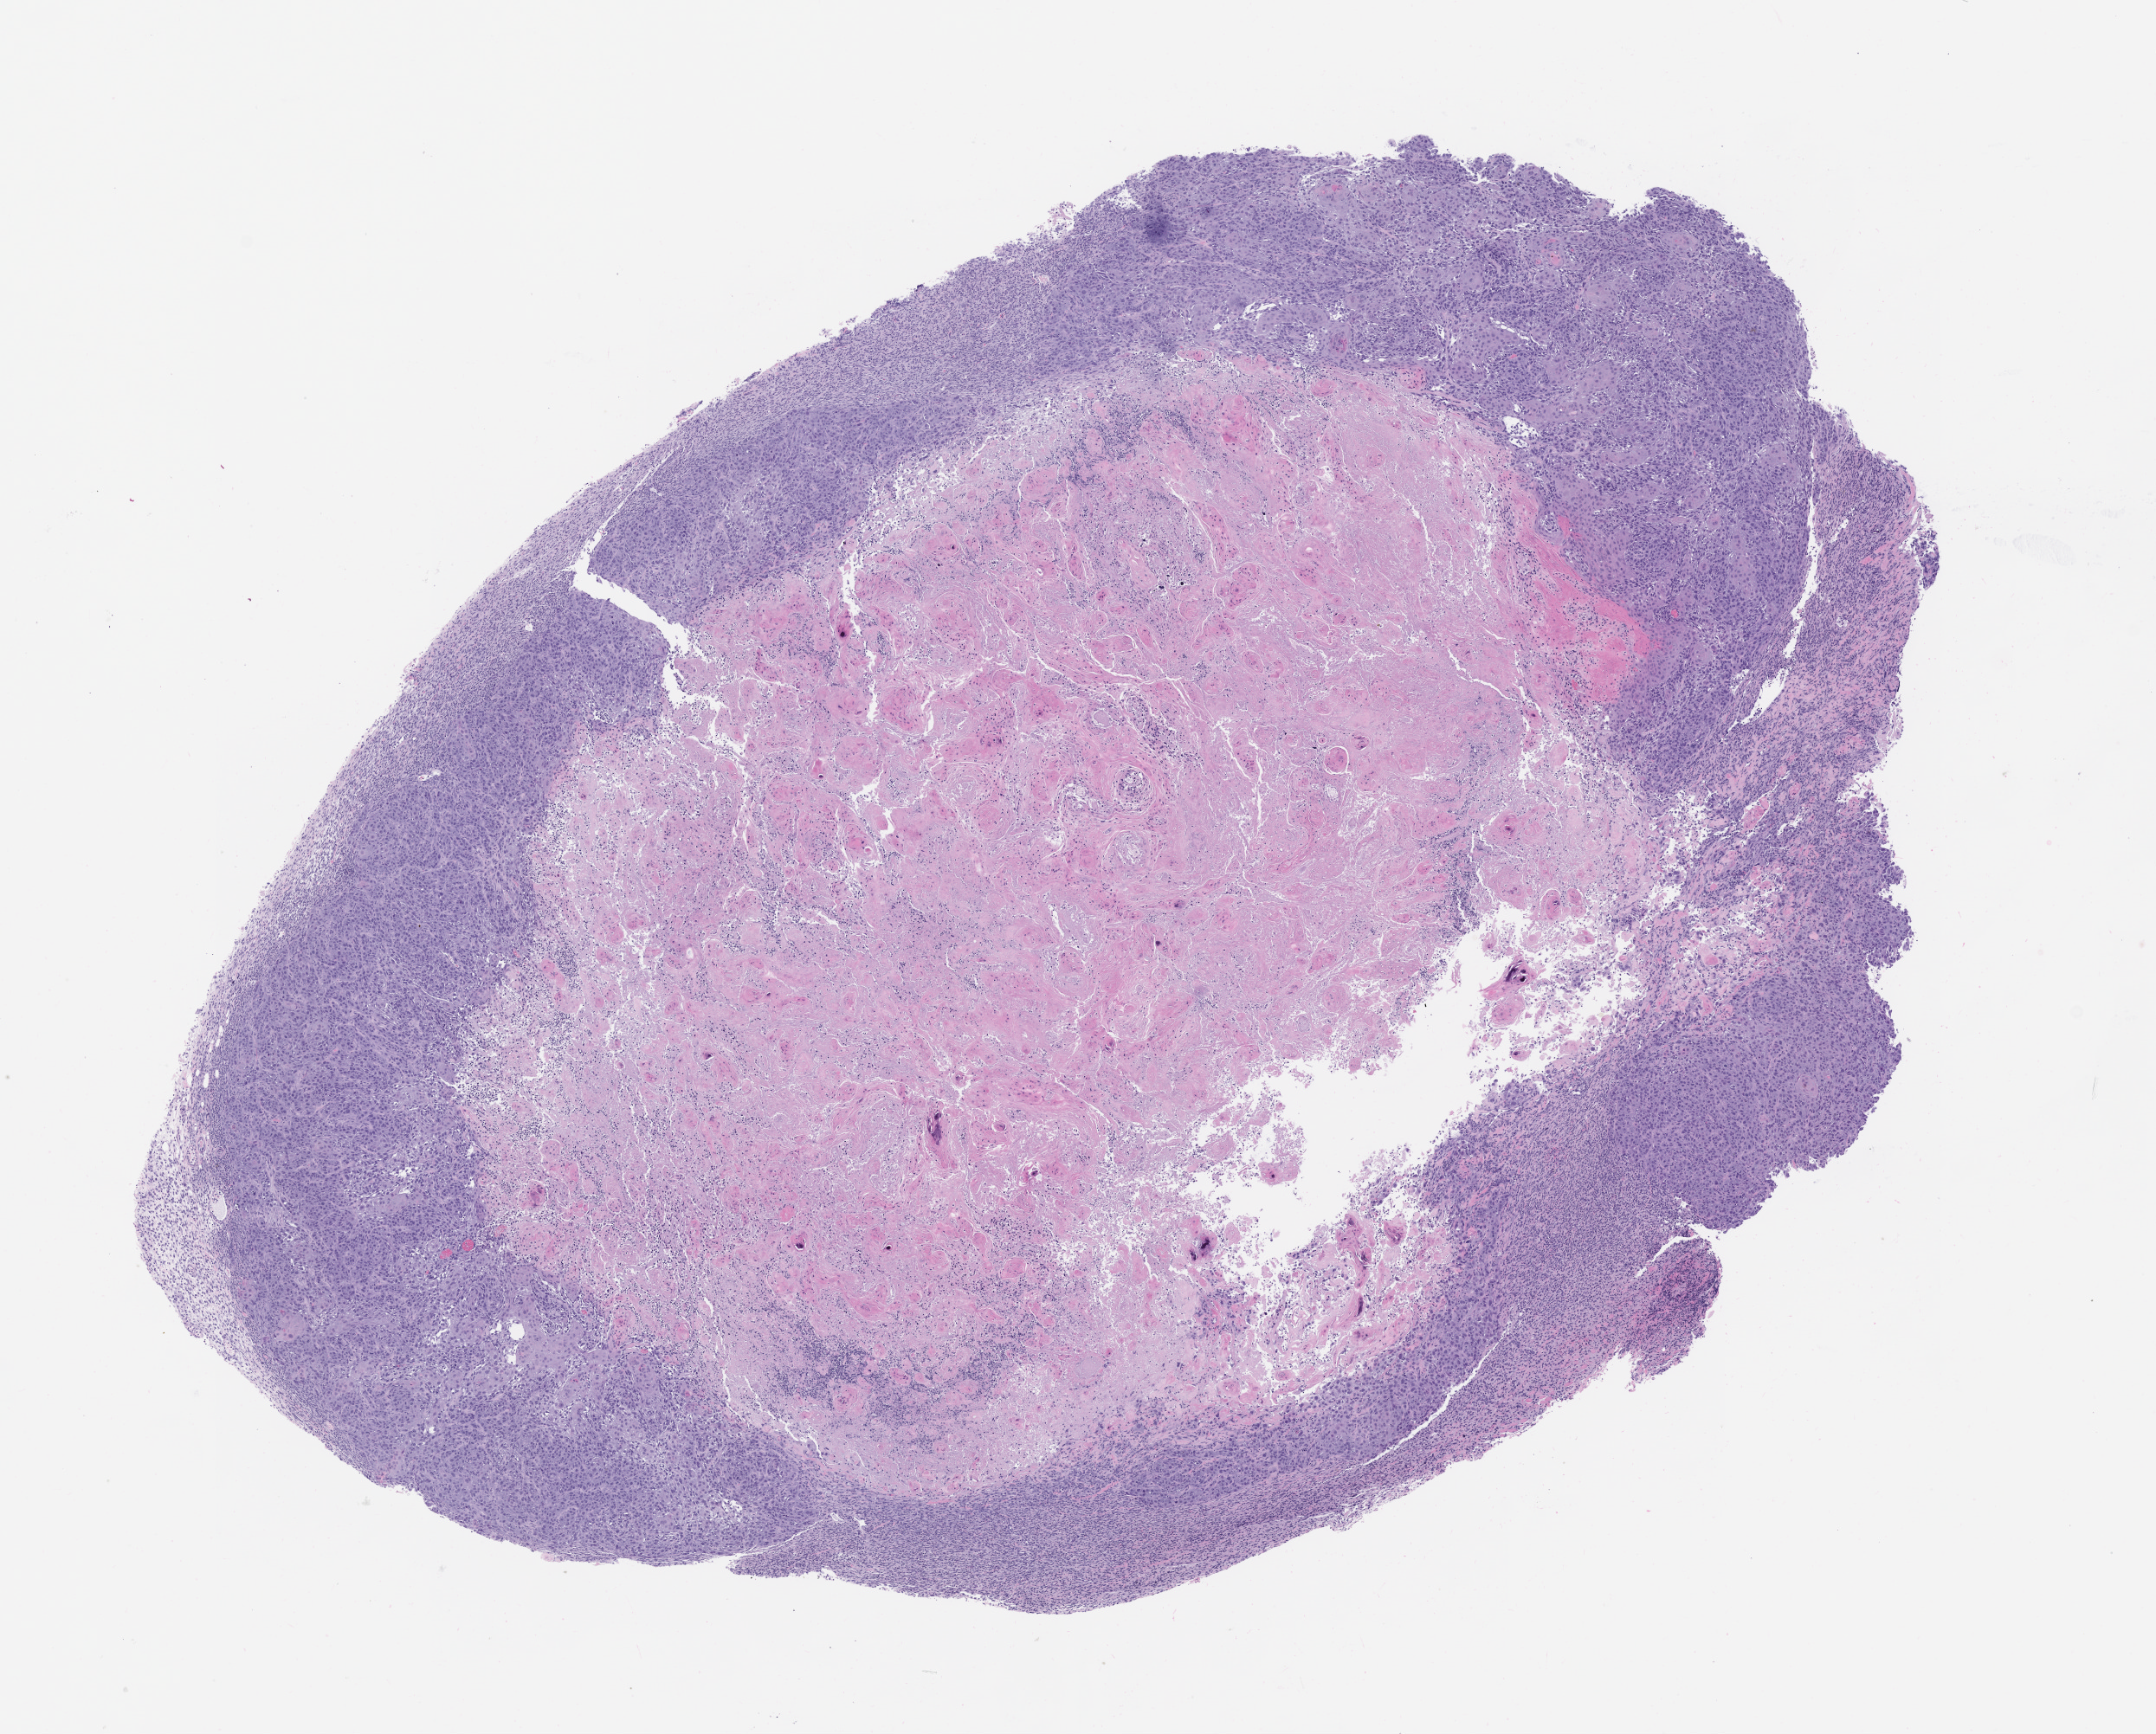
Whole-slide image, H&E: patient-derived xenograft (human tumor grown in a mouse), passage 1 — a low-resolution overview of the entire scanned area, about 10.0 x 8.1 mm, formalin-fixed, paraffin-embedded (FFPE) tissue, tumor site category: oral soft tissue.
Originating patient diagnosis: Head and Neck Squamous Cell Carcinoma.